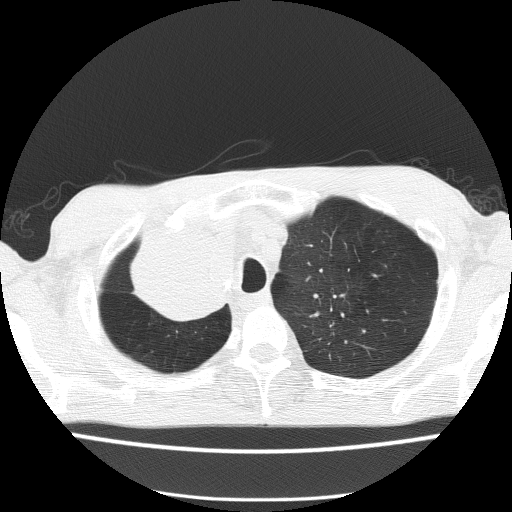
Low-dose screening chest CT, one axial slice; slice 122 of 150 in the series (ordered by position); 120 kVp; lung window (W 1500 / L -600 HU); 512 × 512 image matrix, field of view 336 × 336 mm.
Structures marked on this image (outlined manually by an expert reader):
- lesion 1 (tumor, hilum of right lung): bounding box [x1, y1, x2, y2] px = [132, 223, 225, 319]